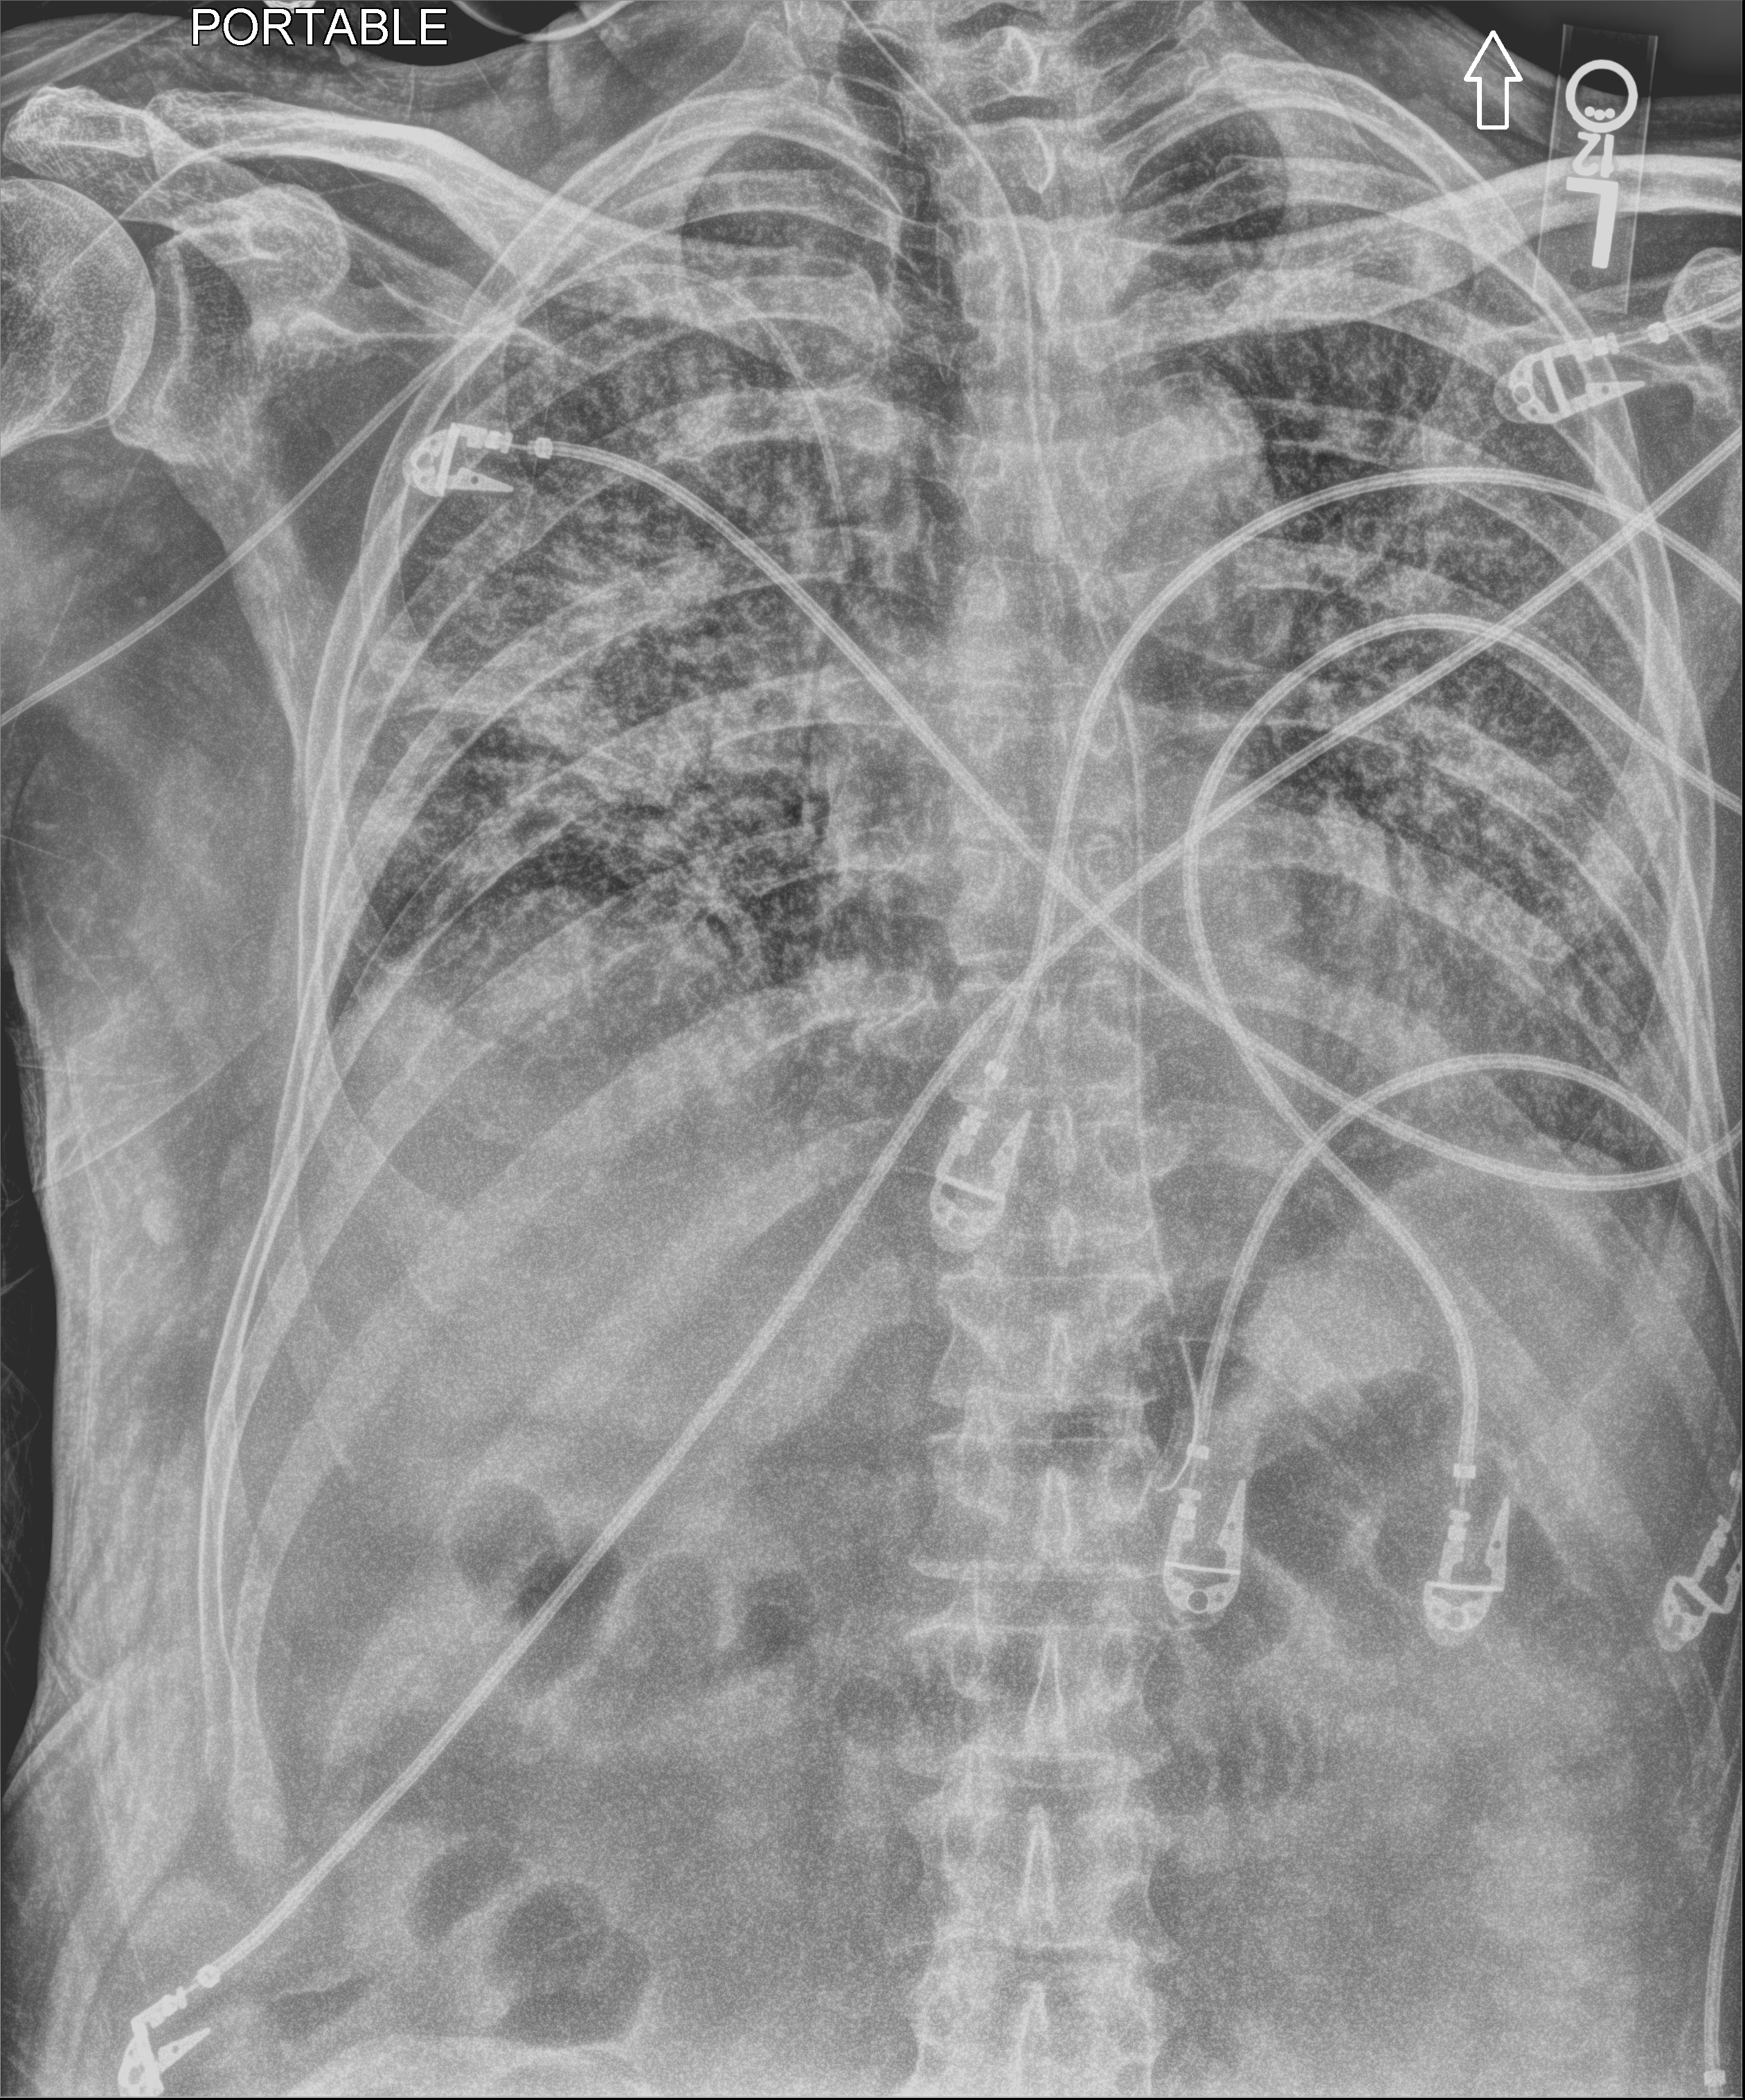
Portable chest radiograph, anteroposterior (AP) projection. Male patient hospitalised with COVID-19, age 60–74 years.
From the hospital-stay record, not from the radiograph (when in the stay this image was taken is not recorded): mechanically ventilated during this hospital stay: yes.